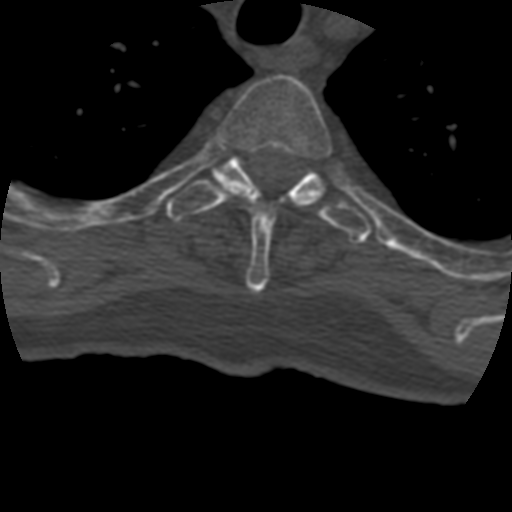
CT including the spine, one axial slice. Slice 345 of 399 in the series (ordered by position). Reconstruction kernel STANDARD. Bone window (W 1800 / L 400 HU). 1.25 mm slice thickness. 512 × 512 image matrix, field of view 160 × 160 mm. Patient age 69 years. Case-level facts recorded for this patient, not image findings: primary cancer: prostate.
Annotated regions visible in this slice (semi-automatic segmentation, software-assisted and operator-edited):
- T3 vertebra: bounding box <212,75,333,293> (left, top, right, bottom; pixels)
- T4 vertebra: <166,155,375,244>